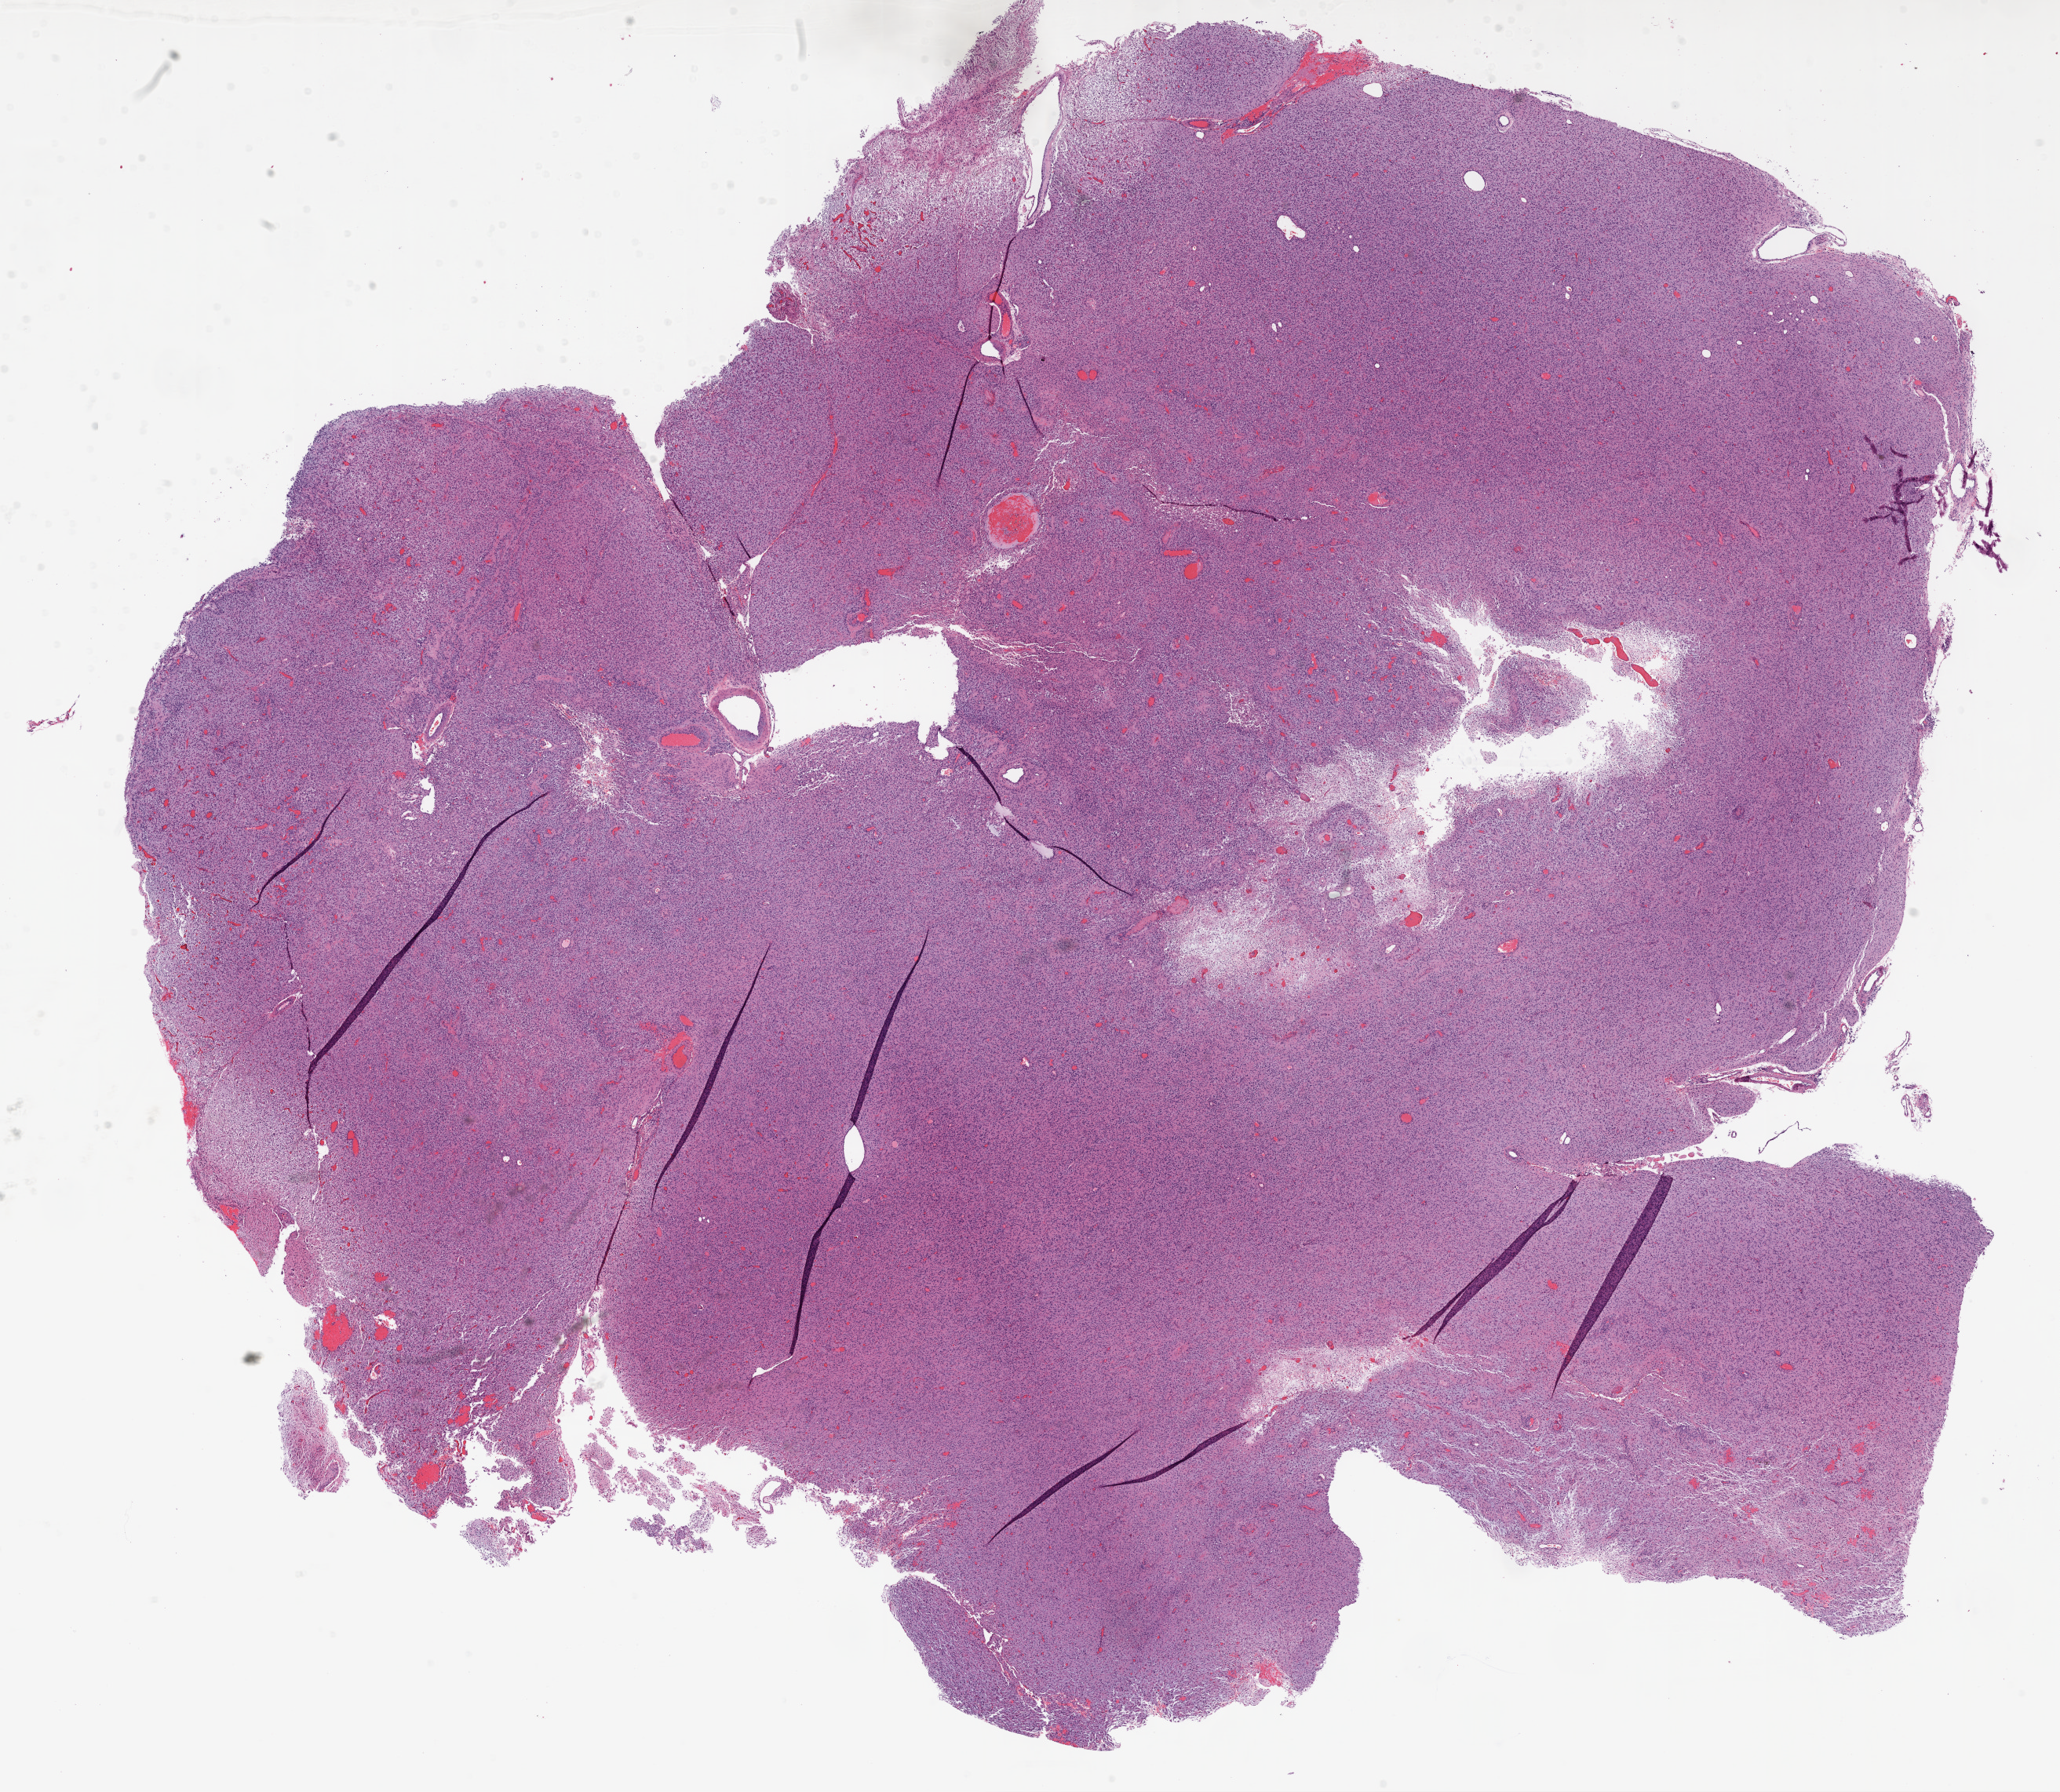
Digitized H&E tissue section (whole slide) — shown as a low-resolution overview of the whole scanned area (about 21.1 x 18.3 mm), FFPE section, primary tumour sample from the brain. Patient: male, age at initial diagnosis 57 years.
Pathologic diagnosis: Glioblastoma.